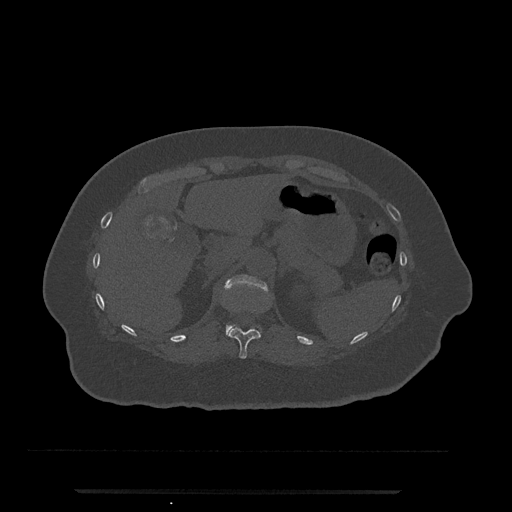
CT including the spine, one axial slice; position 206 of 797 along the scan axis; reconstruction kernel Br40s/3; bone window (W 1800 / L 400 HU); 0.5 mm slice thickness; 512 × 512 image matrix. Female patient, age 51 years. Case-level facts recorded for this patient, not image findings: primary cancer: neuro.
Annotated regions visible in this slice (semi-automatic segmentation, software-assisted and operator-edited):
- T11 vertebra: bounding box <227,327,261,359> (left, top, right, bottom; pixels)
- T12 vertebra: <225,274,268,335>